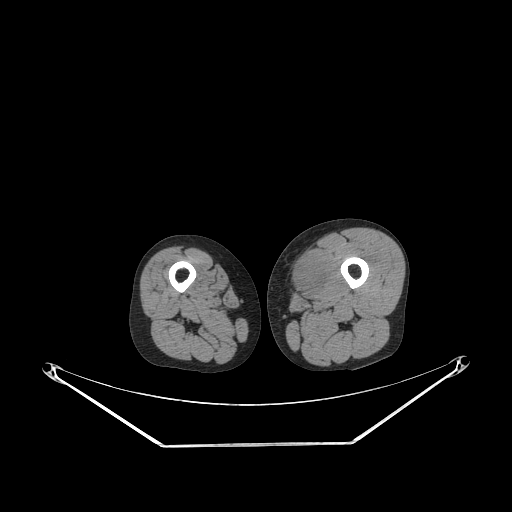
CT of an extremity soft-tissue mass (from a PET/CT study), one axial slice; slice 224 of 267 in the series (ordered by position); reconstruction kernel STANDARD; 140 kVp; soft-tissue window (W 400 / L 40 HU); 512 × 512 image matrix, field of view 500 × 500 mm. Male patient. From the clinical record (not read from this slice): histological type: pleiomorphic leiomyosarcoma; grade: high; site of the primary tumour: left thigh.
Outlined on this slice (expert contour drawn on MRI and transferred to this co-registered scan by the dataset authors):
- gross tumour volume including surrounding oedema: bounding box (x1, y1, x2, y2) in pixels: (288, 251, 328, 296)
- gross tumour volume (mass): (290, 254, 323, 293)